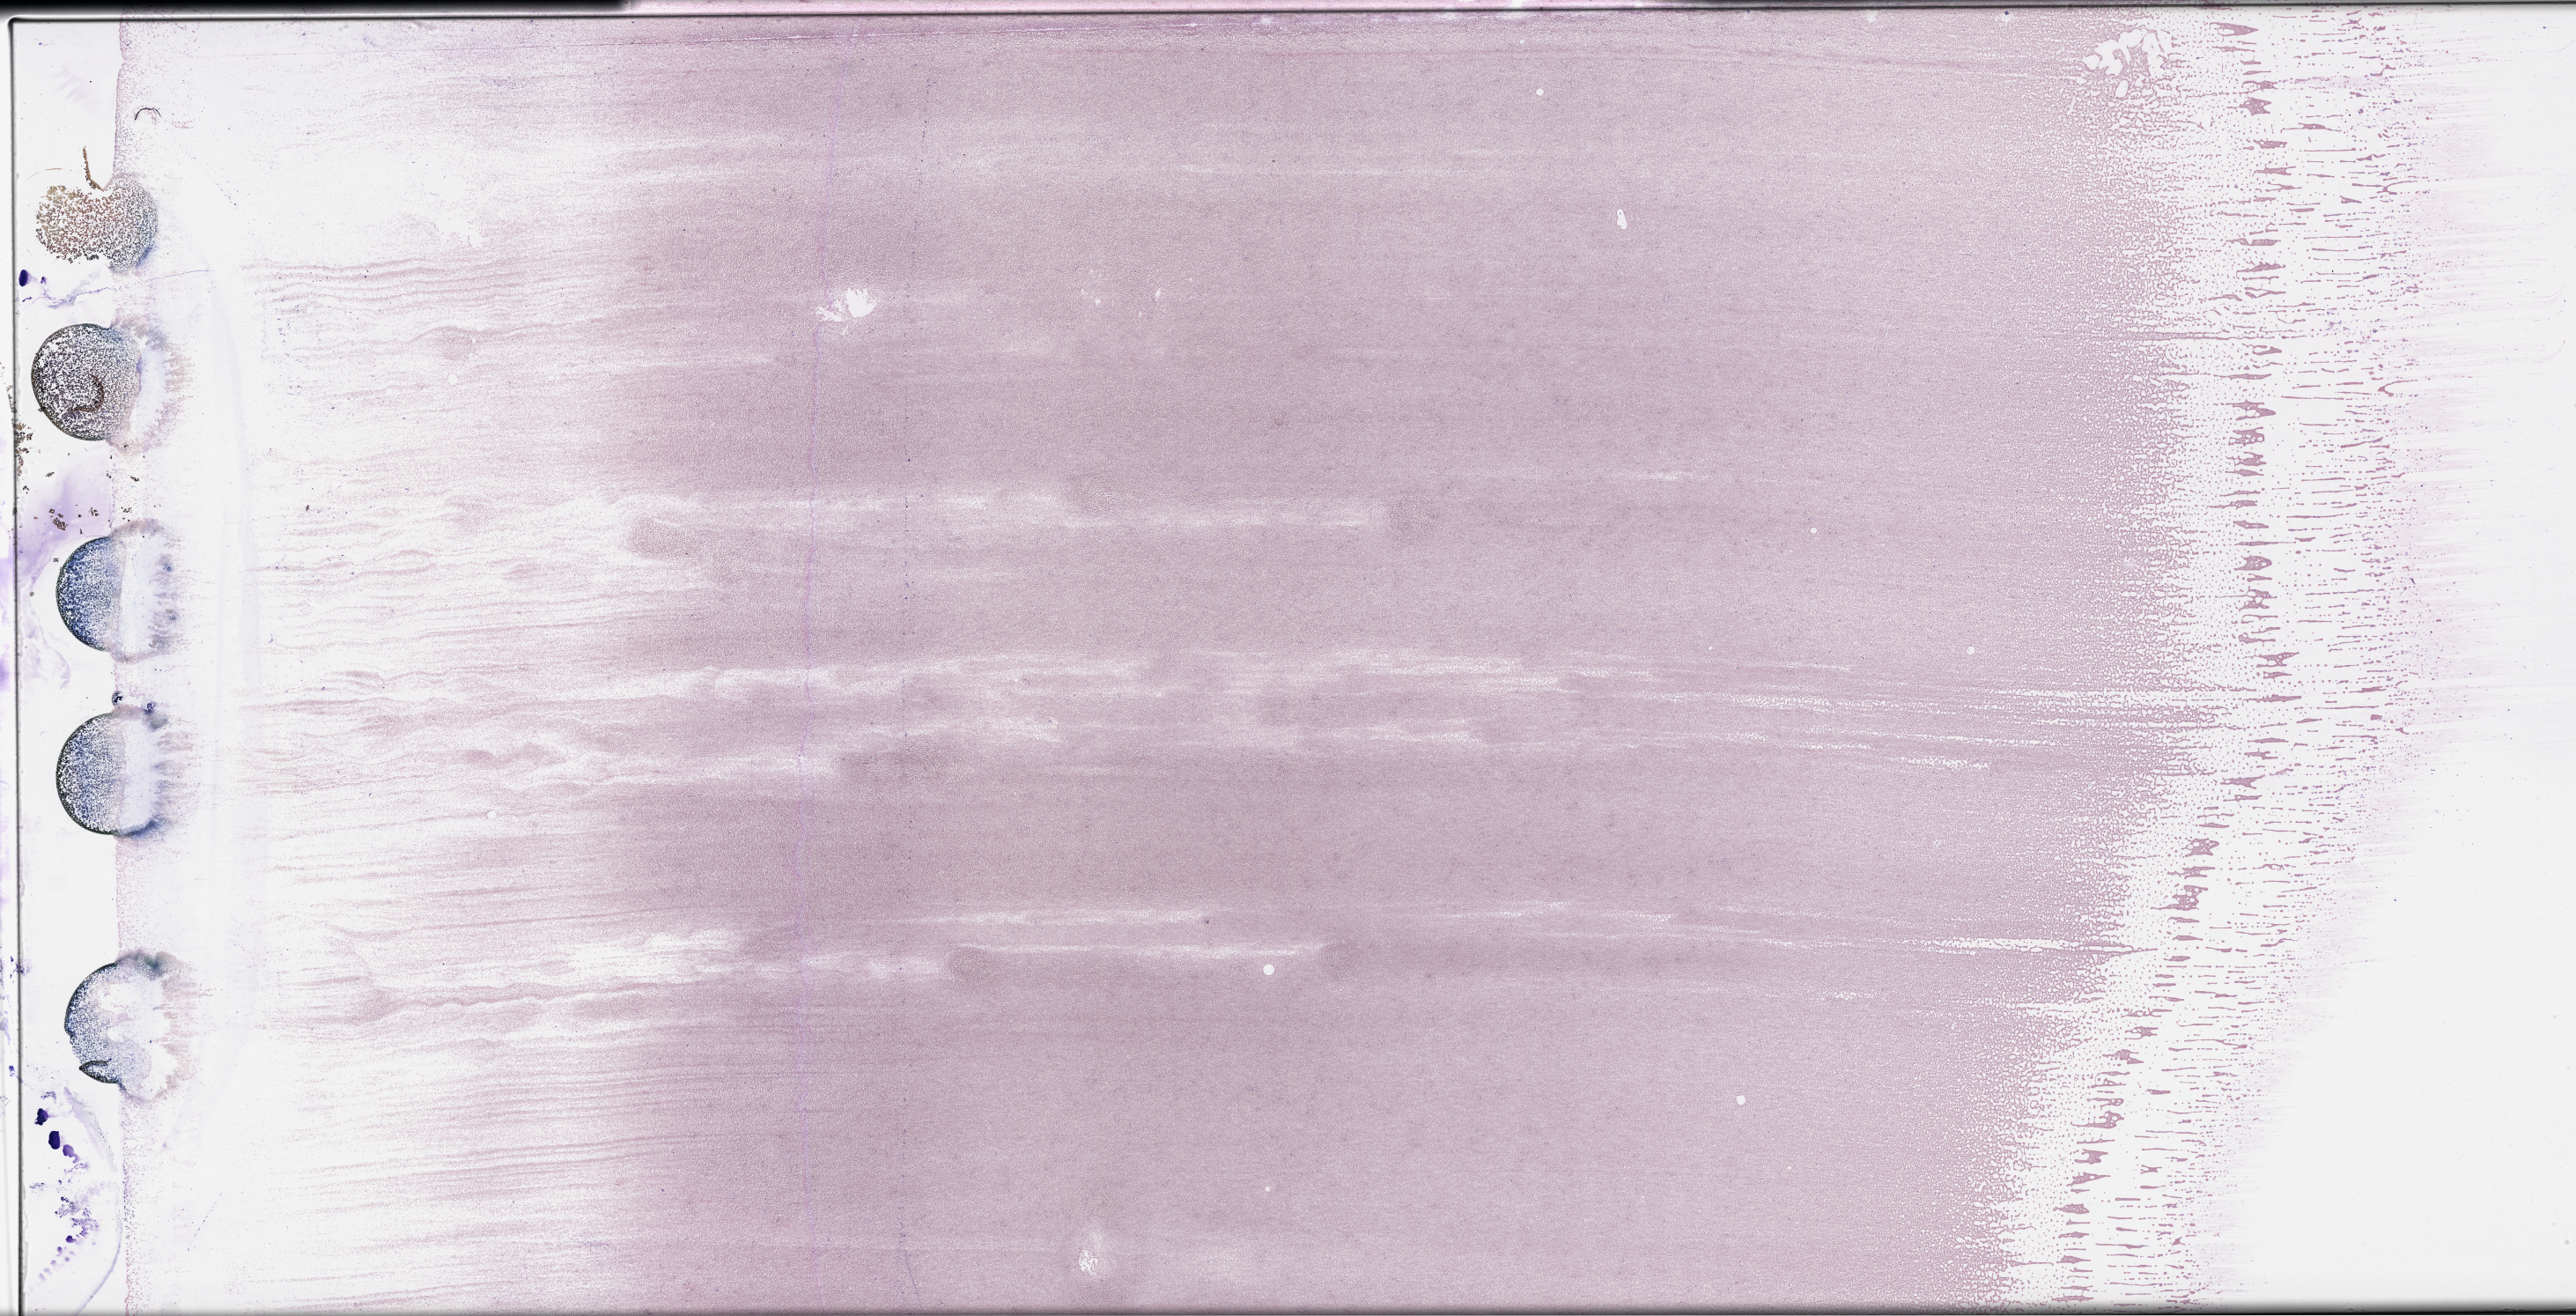
Digitized H&E-stained tissue section (whole slide) — a low-resolution overview of the entire scanned area, about 47.2 x 24.1 mm (slide scanned at 40x). Peripheral blood (leukaemic) sample. Female, 41 y/o.
- FAB classification: M5
- diagnosis: Acute Myeloid Leukemia